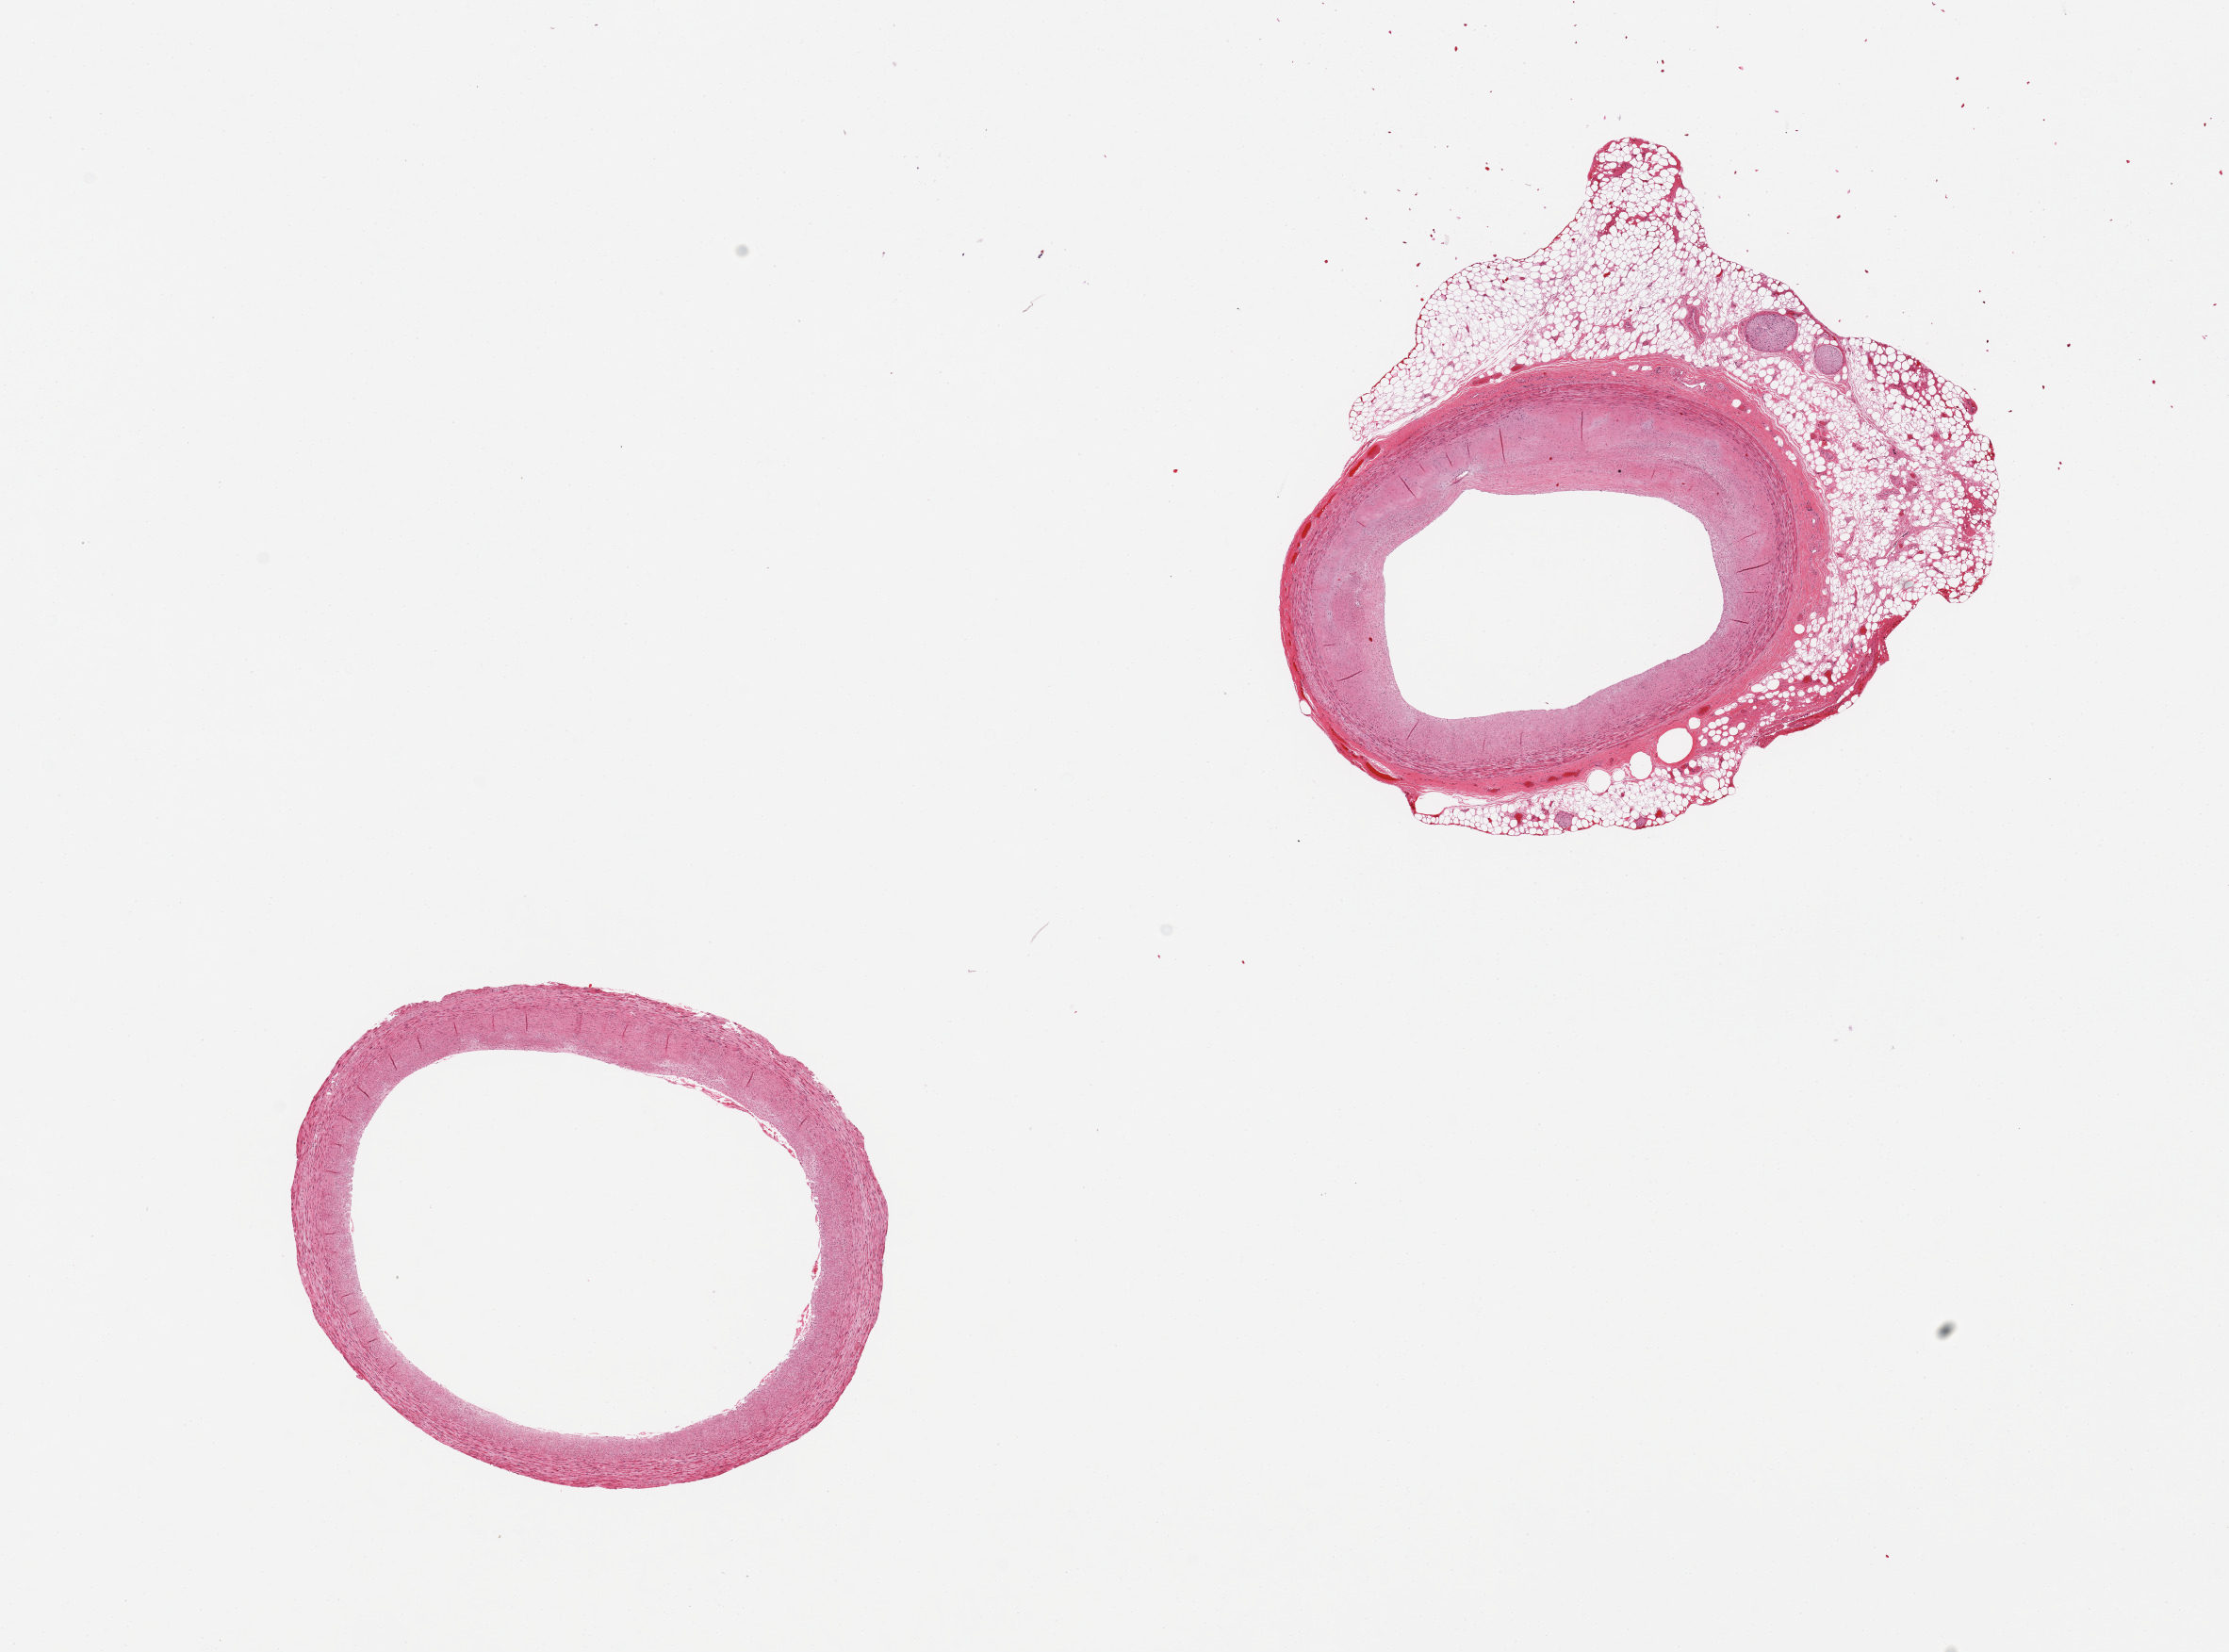
Whole-slide image, haematoxylin and eosin stain, brightfield — a low-resolution overview of the entire scanned area, about 18.7 x 13.9 mm (slide scanned at 20x). PAXgene-fixed, paraffin-embedded tissue. Section of coronary artery (target tissue). Donor tissue sample.
* review note (as recorded): 2 pieces, one is well trimmed, second has attachment of adipose tissue and nerve up to 1.8mm